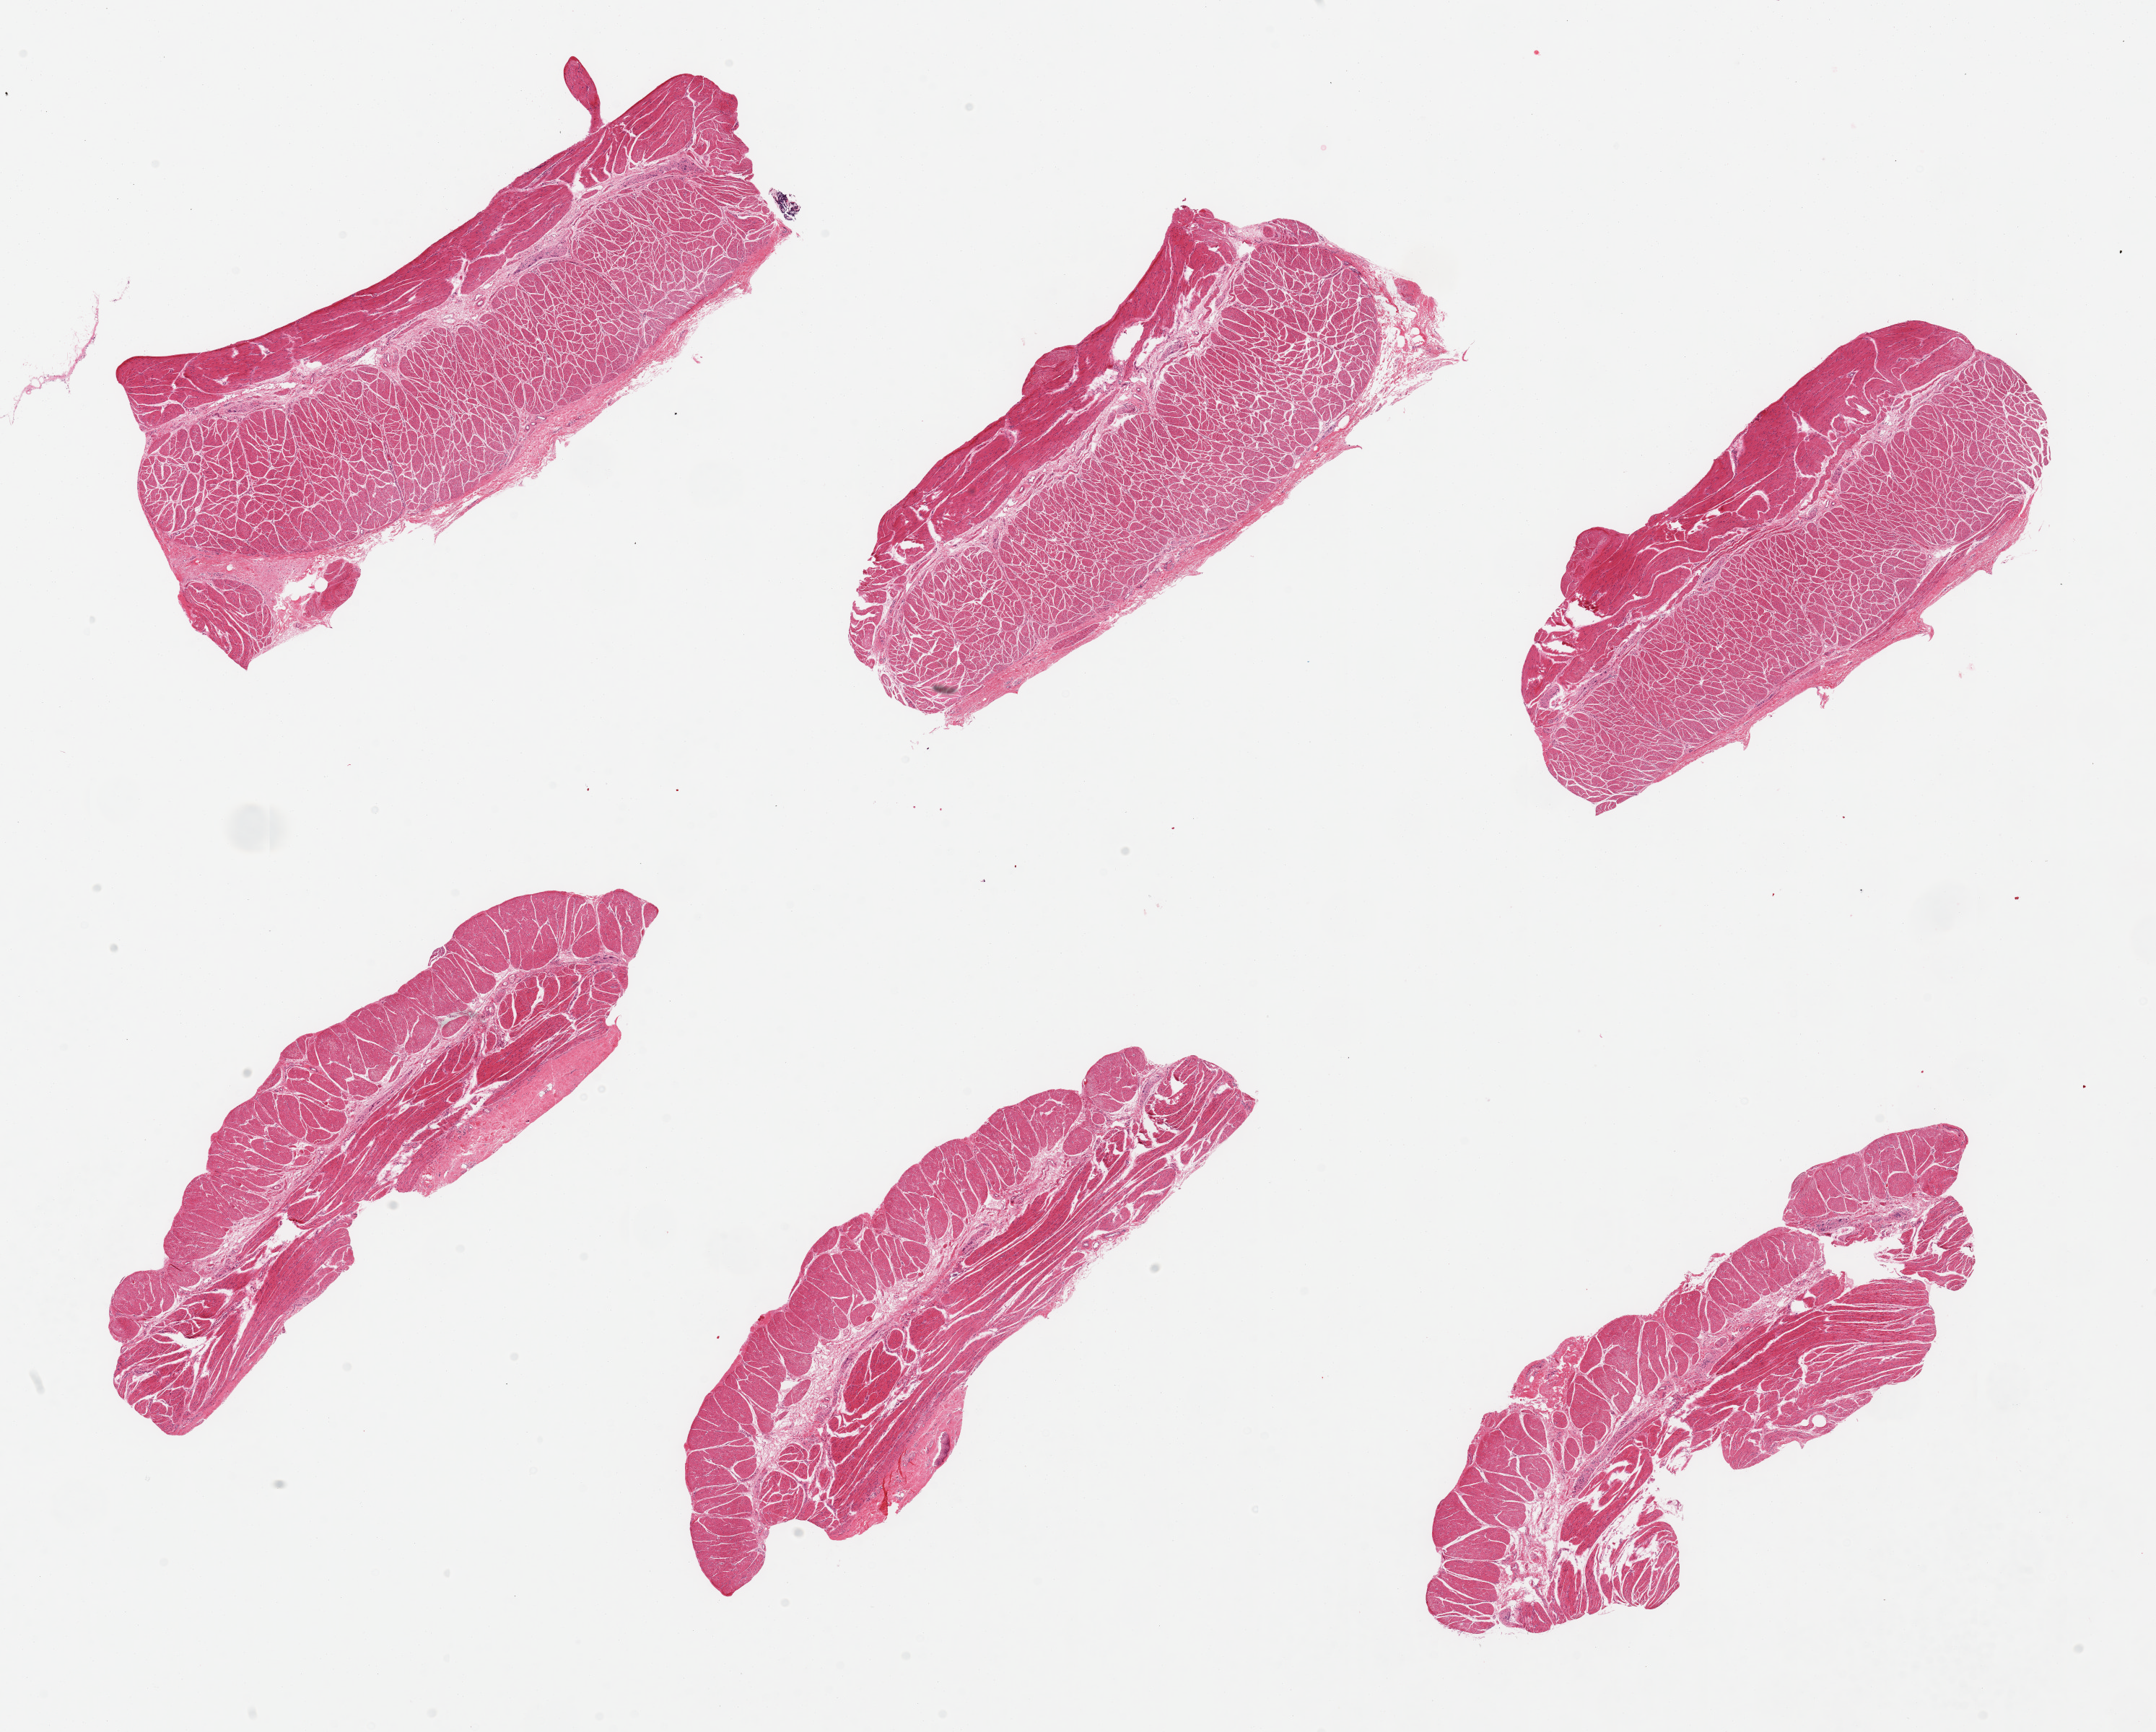
Hematoxylin and eosin (H&E) whole-slide image, shown as a low-resolution overview of the whole scanned area (about 23.6 x 19.0 mm), PAXgene-fixed paraffin-embedded (PFPE) section, section of esophageal muscle (target tissue), tissue donor sample. Donor sex: male.
• pathologist's review note for this sample: 6 pieces, target muscularis, good specimens